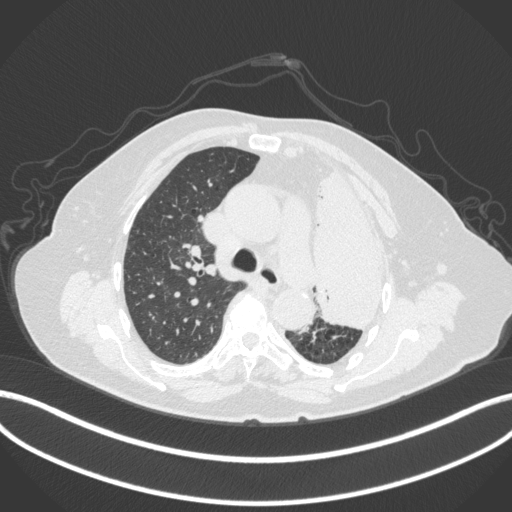
Chest CT, one axial slice. Position 268 of 399 along the scan axis. Reconstruction kernel B31f. Lung window (W 1500 / L -600 HU). 1 mm slice thickness. 512 × 512 image matrix, field of view 400 × 400 mm. Female patient, age 75 years. From the clinical record (not read from this slice): clinical TNM (as recorded): T3 N3 M1.
Annotated regions visible in this slice (rectangle marked by the reading radiologist):
- lung tumour (recorded histology: adenocarcinoma): box from (x=310, y=164) to (x=394, y=327) px